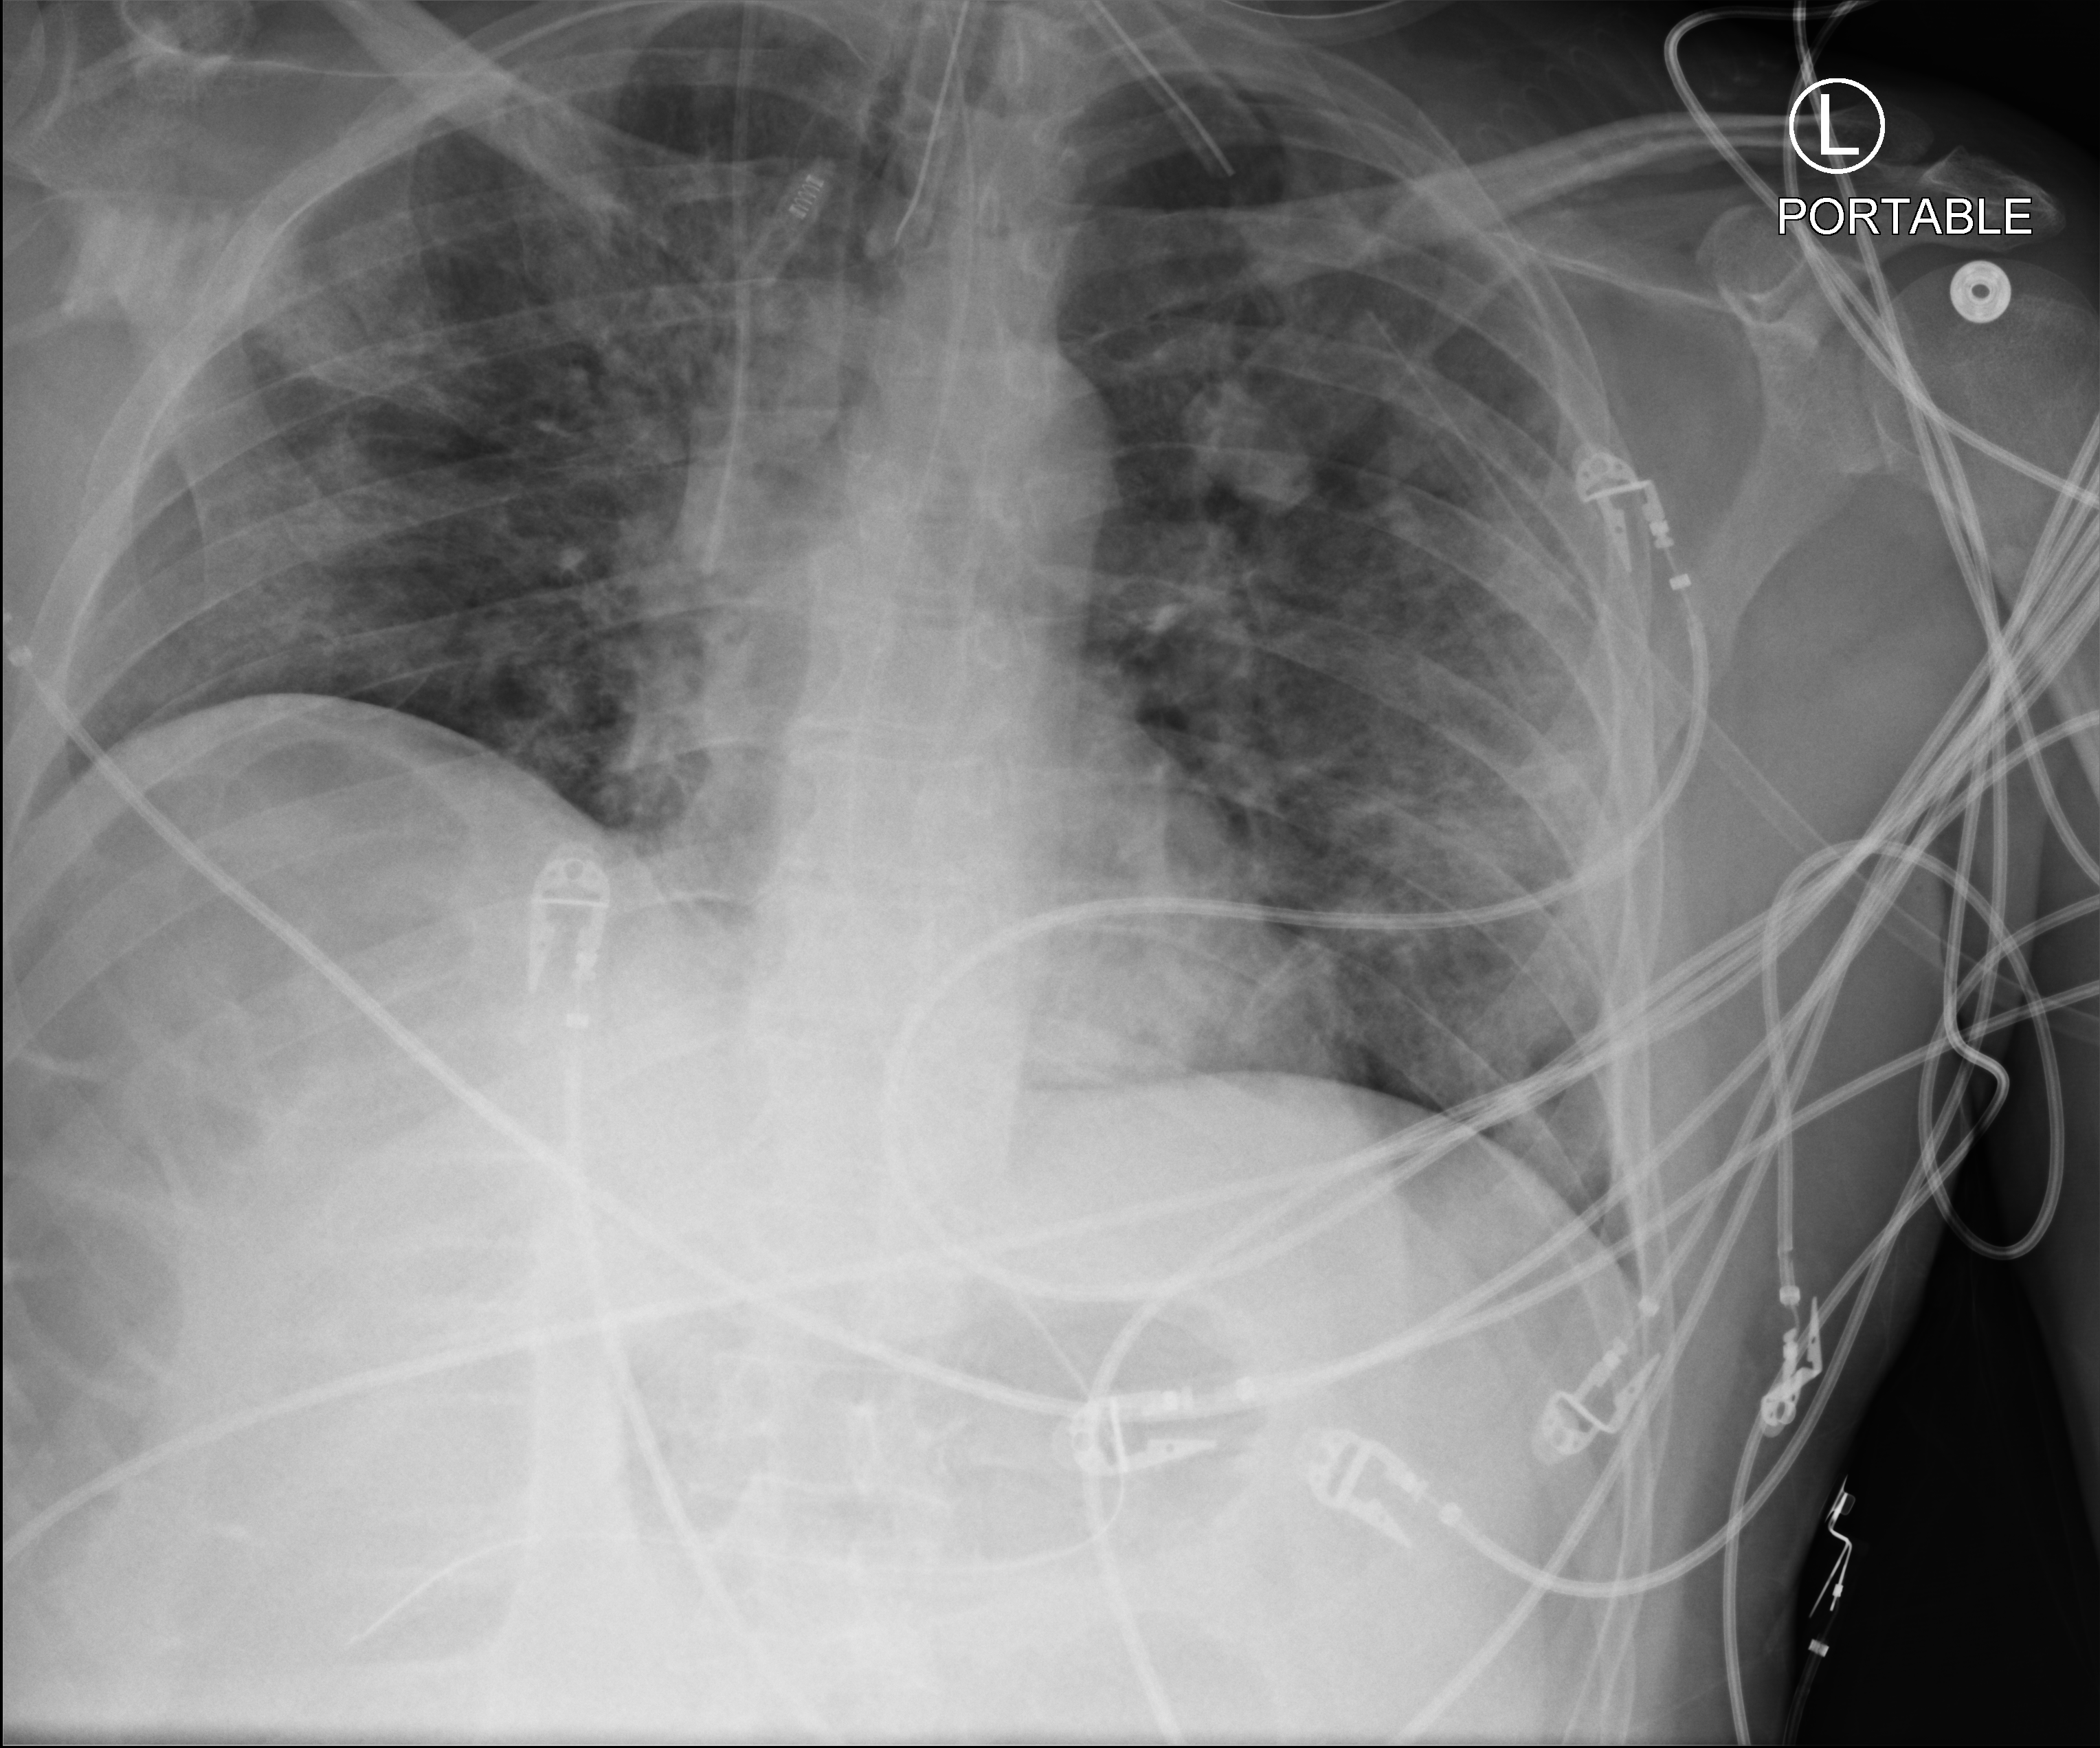
Bedside chest radiograph (computed radiography), anteroposterior (AP) projection. Male patient hospitalised with COVID-19, age 18–59 years.
Hospital-stay facts (about this admission, not read from this image; timing relative to this image not recorded): admitted to intensive care during this hospital stay: yes.